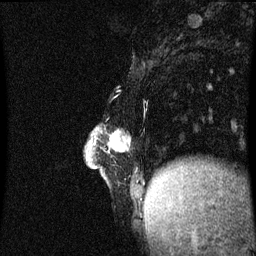
Breast MRI (dynamic contrast-enhanced), one sagittal slice. Position 15 of 60 along the scan axis. Dynamic contrast-enhanced series, image 2 of 3 at this slice position (ordered by acquisition). 1.5 T. TE 4.2 ms, TR 8.9 ms. 2 mm slice thickness. 256 × 256 image matrix. Female patient, age 47 years. From the clinical record (not read from this slice): setting: breast cancer imaged before/during neoadjuvant chemotherapy; receptor status: HR-positive, HER2-negative.
Annotated regions visible in this slice (semi-automatic segmentation, software-assisted and operator-edited):
- analysis volume of interest (the breast-tissue region the enhancement analysis was run in; not a lesion): box from (x=88, y=128) to (x=146, y=199) px
- tumour enhancement mask (voxels above the 70 % enhancement threshold inside the analysis volume of interest): (x=114, y=134)–(x=125, y=149)